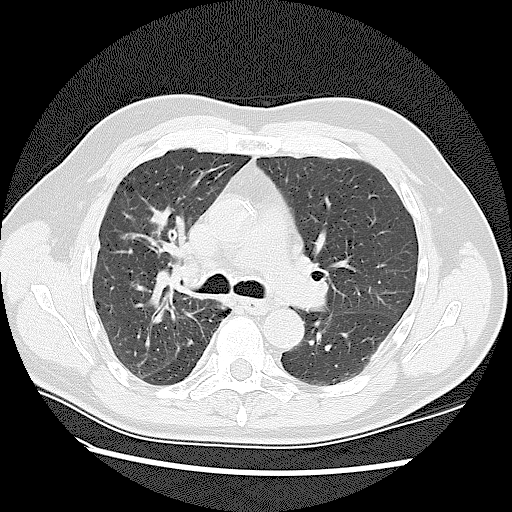
Low-dose screening chest CT, one axial slice. 120 kVp. Lung window (W 1500 / L -600 HU). 512 × 512 image matrix.
Structures marked on this image (expert manual segmentation):
- lesion 1 (tumor, upper lobe of right lung): bounding box [x1, y1, x2, y2] px = [151, 210, 170, 230]